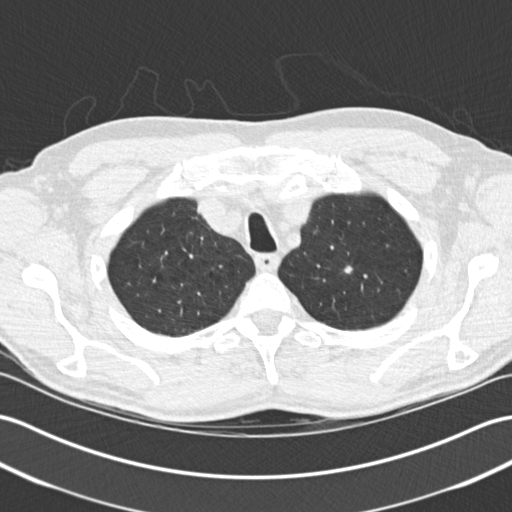
Low-dose screening chest CT, axial slice, first (baseline) screen, lung window (W 1500 / L -600 HU), standard (soft-tissue) reconstruction kernel (B30f), 120 kVp, slice 38 of 205 in the series. Male, age 64 years at enrolment. Former smoker at enrolment.
Expert-annotated lung lesion, box from (x=330, y=256) to (x=364, y=287) px. The exam's reader record, not a measurement of the box and not confirmed to be the same lesion: non-calcified nodule or mass ≥4 mm, right upper lobe, 7 × 5 mm, spiculated (stellate) margins, soft tissue attenuation. Note: the box lies in the patient's left hemithorax on this image, whereas the reader's record names the right lung; they may be different findings. Participant outcome: lung cancer diagnosed 833 days after this screen (after the third annual screen) — adenocarcinoma, NOS, left upper lobe, poorly differentiated (G3), stage IA (AJCC 6th edition), 10 mm at pathology.